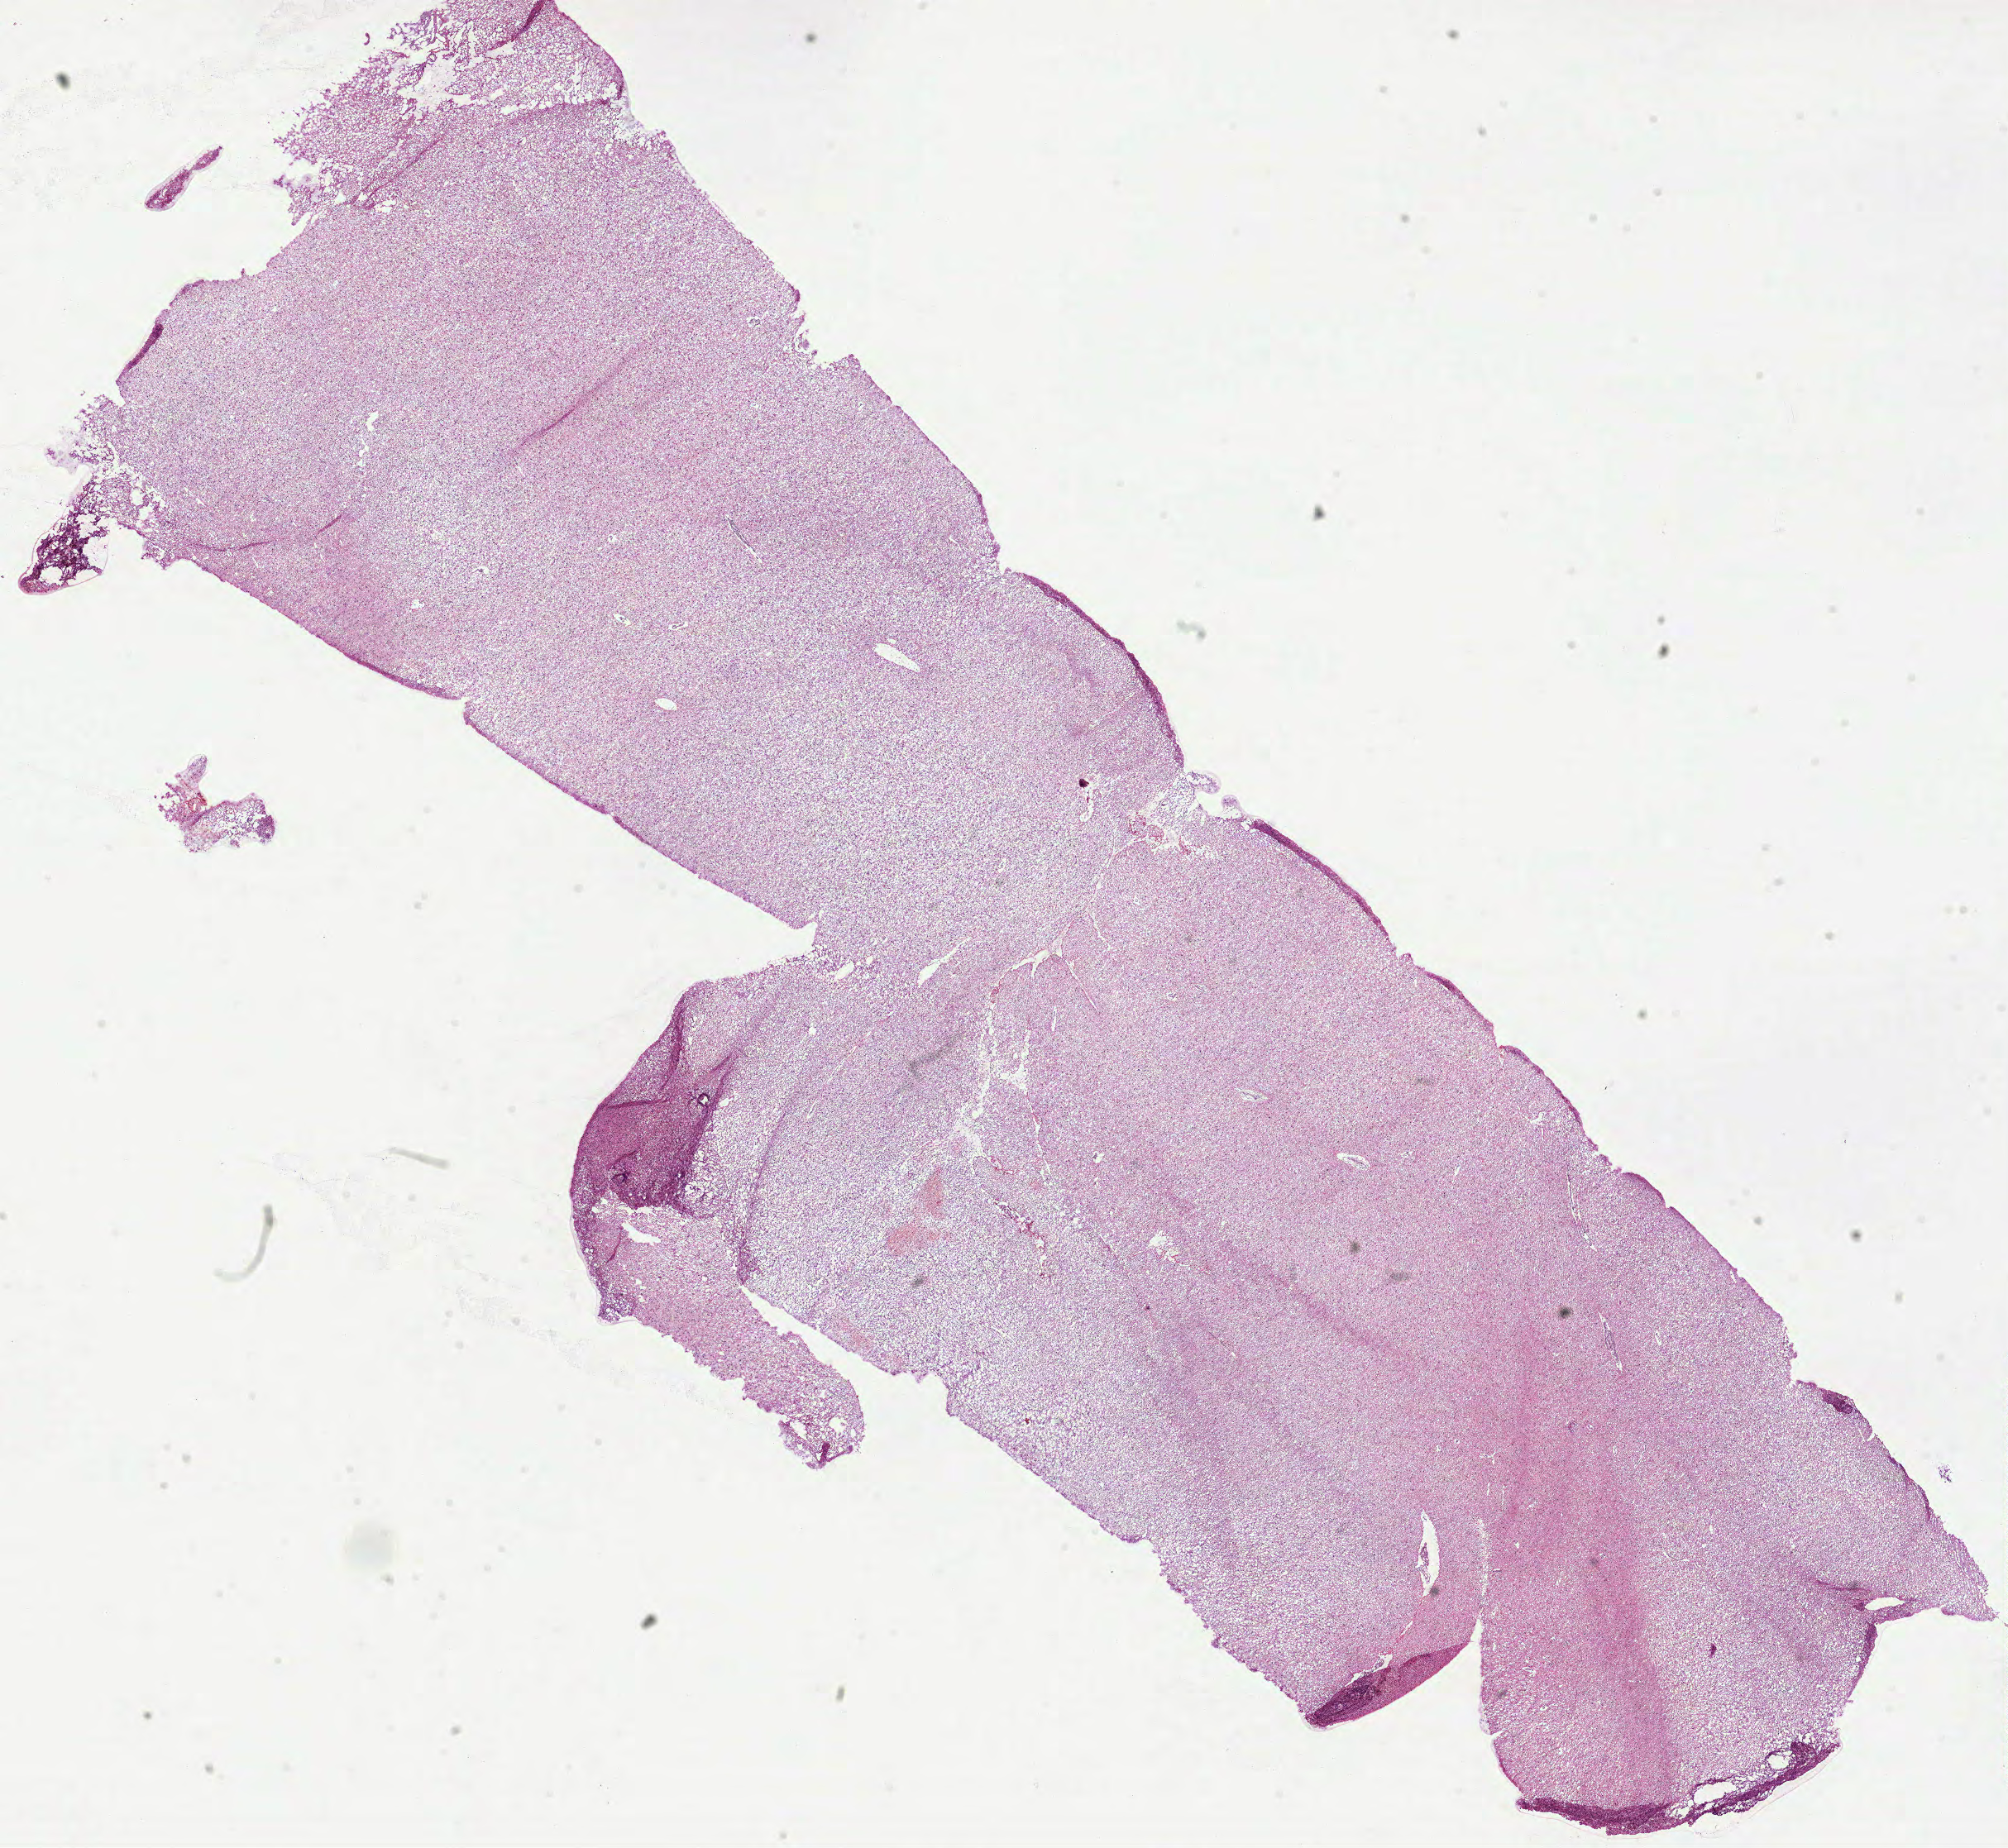
Digitized H&E tissue section (whole slide), low-resolution overview of the scanned area, about 19.6 x 18.0 mm (from a 40x scan), frozen section, primary tumour sample from the brain. Male patient; age at initial diagnosis 38 years. Histologic grade: G2 (moderately differentiated). Pathologist review of this section (percent, as recorded): tumour cells 100%, tumour nuclei 65%, normal cells 0%, stromal cells 0%, necrosis 0%.
Pathologic diagnosis: Oligodendroglioma, NOS (cerebrum).